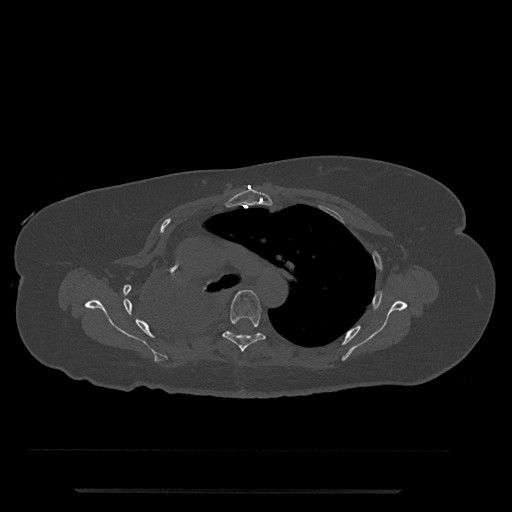
CT including the spine, one axial slice. Slice 543 of 797 in the series (ordered by position). Bone window (W 1800 / L 400 HU). 512 × 512 image matrix. Female patient, age 51 years. From the clinical record (not read from this slice): primary cancer: neuro; vertebrae with lytic lesions (as recorded): T8.
Annotated regions visible in this slice (semi-automatically segmented with operator editing):
- T5 vertebra: bounding box <222,290,266,352> (left, top, right, bottom; pixels)